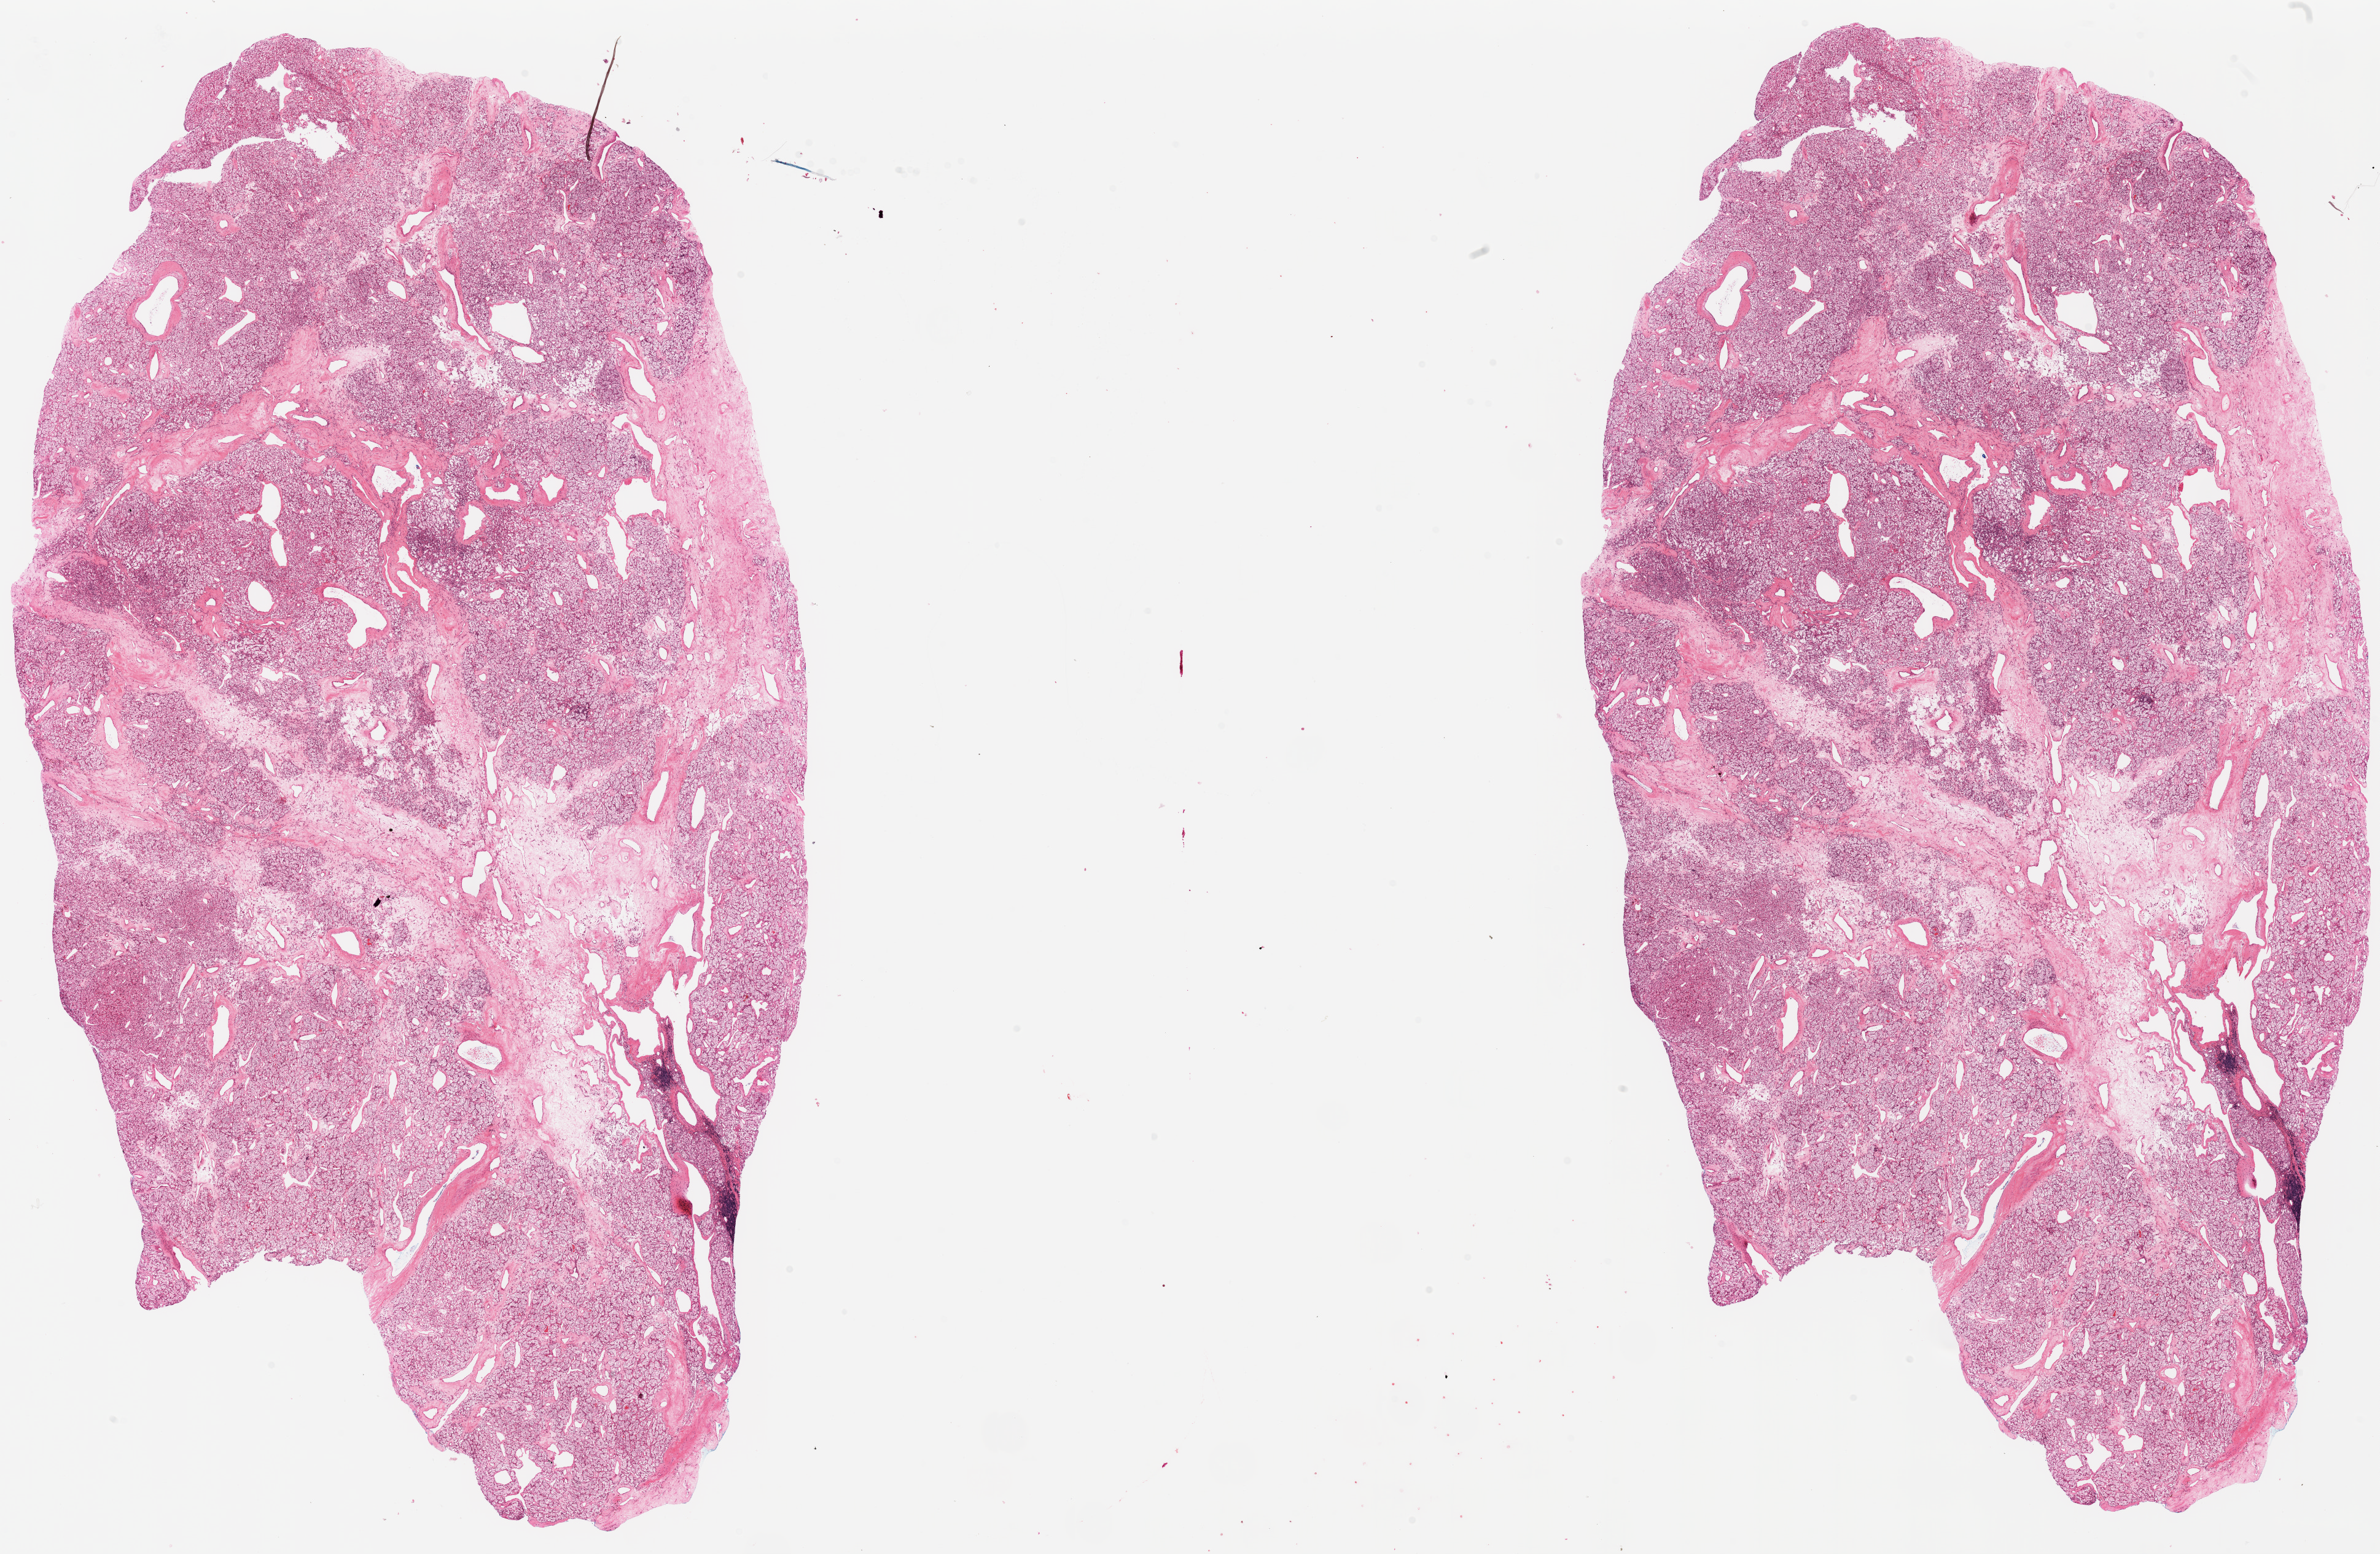
Digitized Hematoxylin and eosin (H&E) stained tissue section (whole slide), a low-resolution overview of the entire scanned area, about 30.6 x 20.0 mm; formalin-fixed paraffin-embedded (FFPE) diagnostic section; primary tumour sample from the kidney. Male patient; age at initial diagnosis 43 years. Histologic grade: G2 (moderately differentiated).
AJCC pathologic stage: I. Laterality: right. Histologic diagnosis: Clear cell adenocarcinoma, NOS.